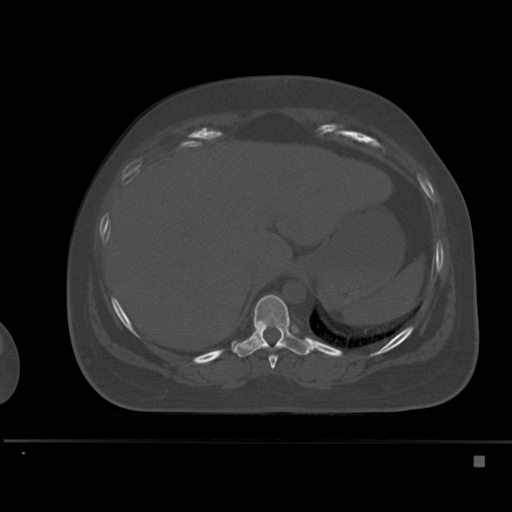
CT including the spine, one axial slice. Slice 251 of 495 in the series (ordered by position). Bone window (W 1800 / L 400 HU). 1.5 mm slice thickness. 512 × 512 image matrix, field of view 404 × 404 mm. Patient: female, 33 years. From the clinical record (not read from this slice): primary cancer: breast.
Outlined on this slice (semi-automatically segmented with operator editing):
- T10 vertebra: bounding box [x1, y1, x2, y2] px = [233, 294, 312, 358]
- T9 vertebra: [269, 355, 278, 369]